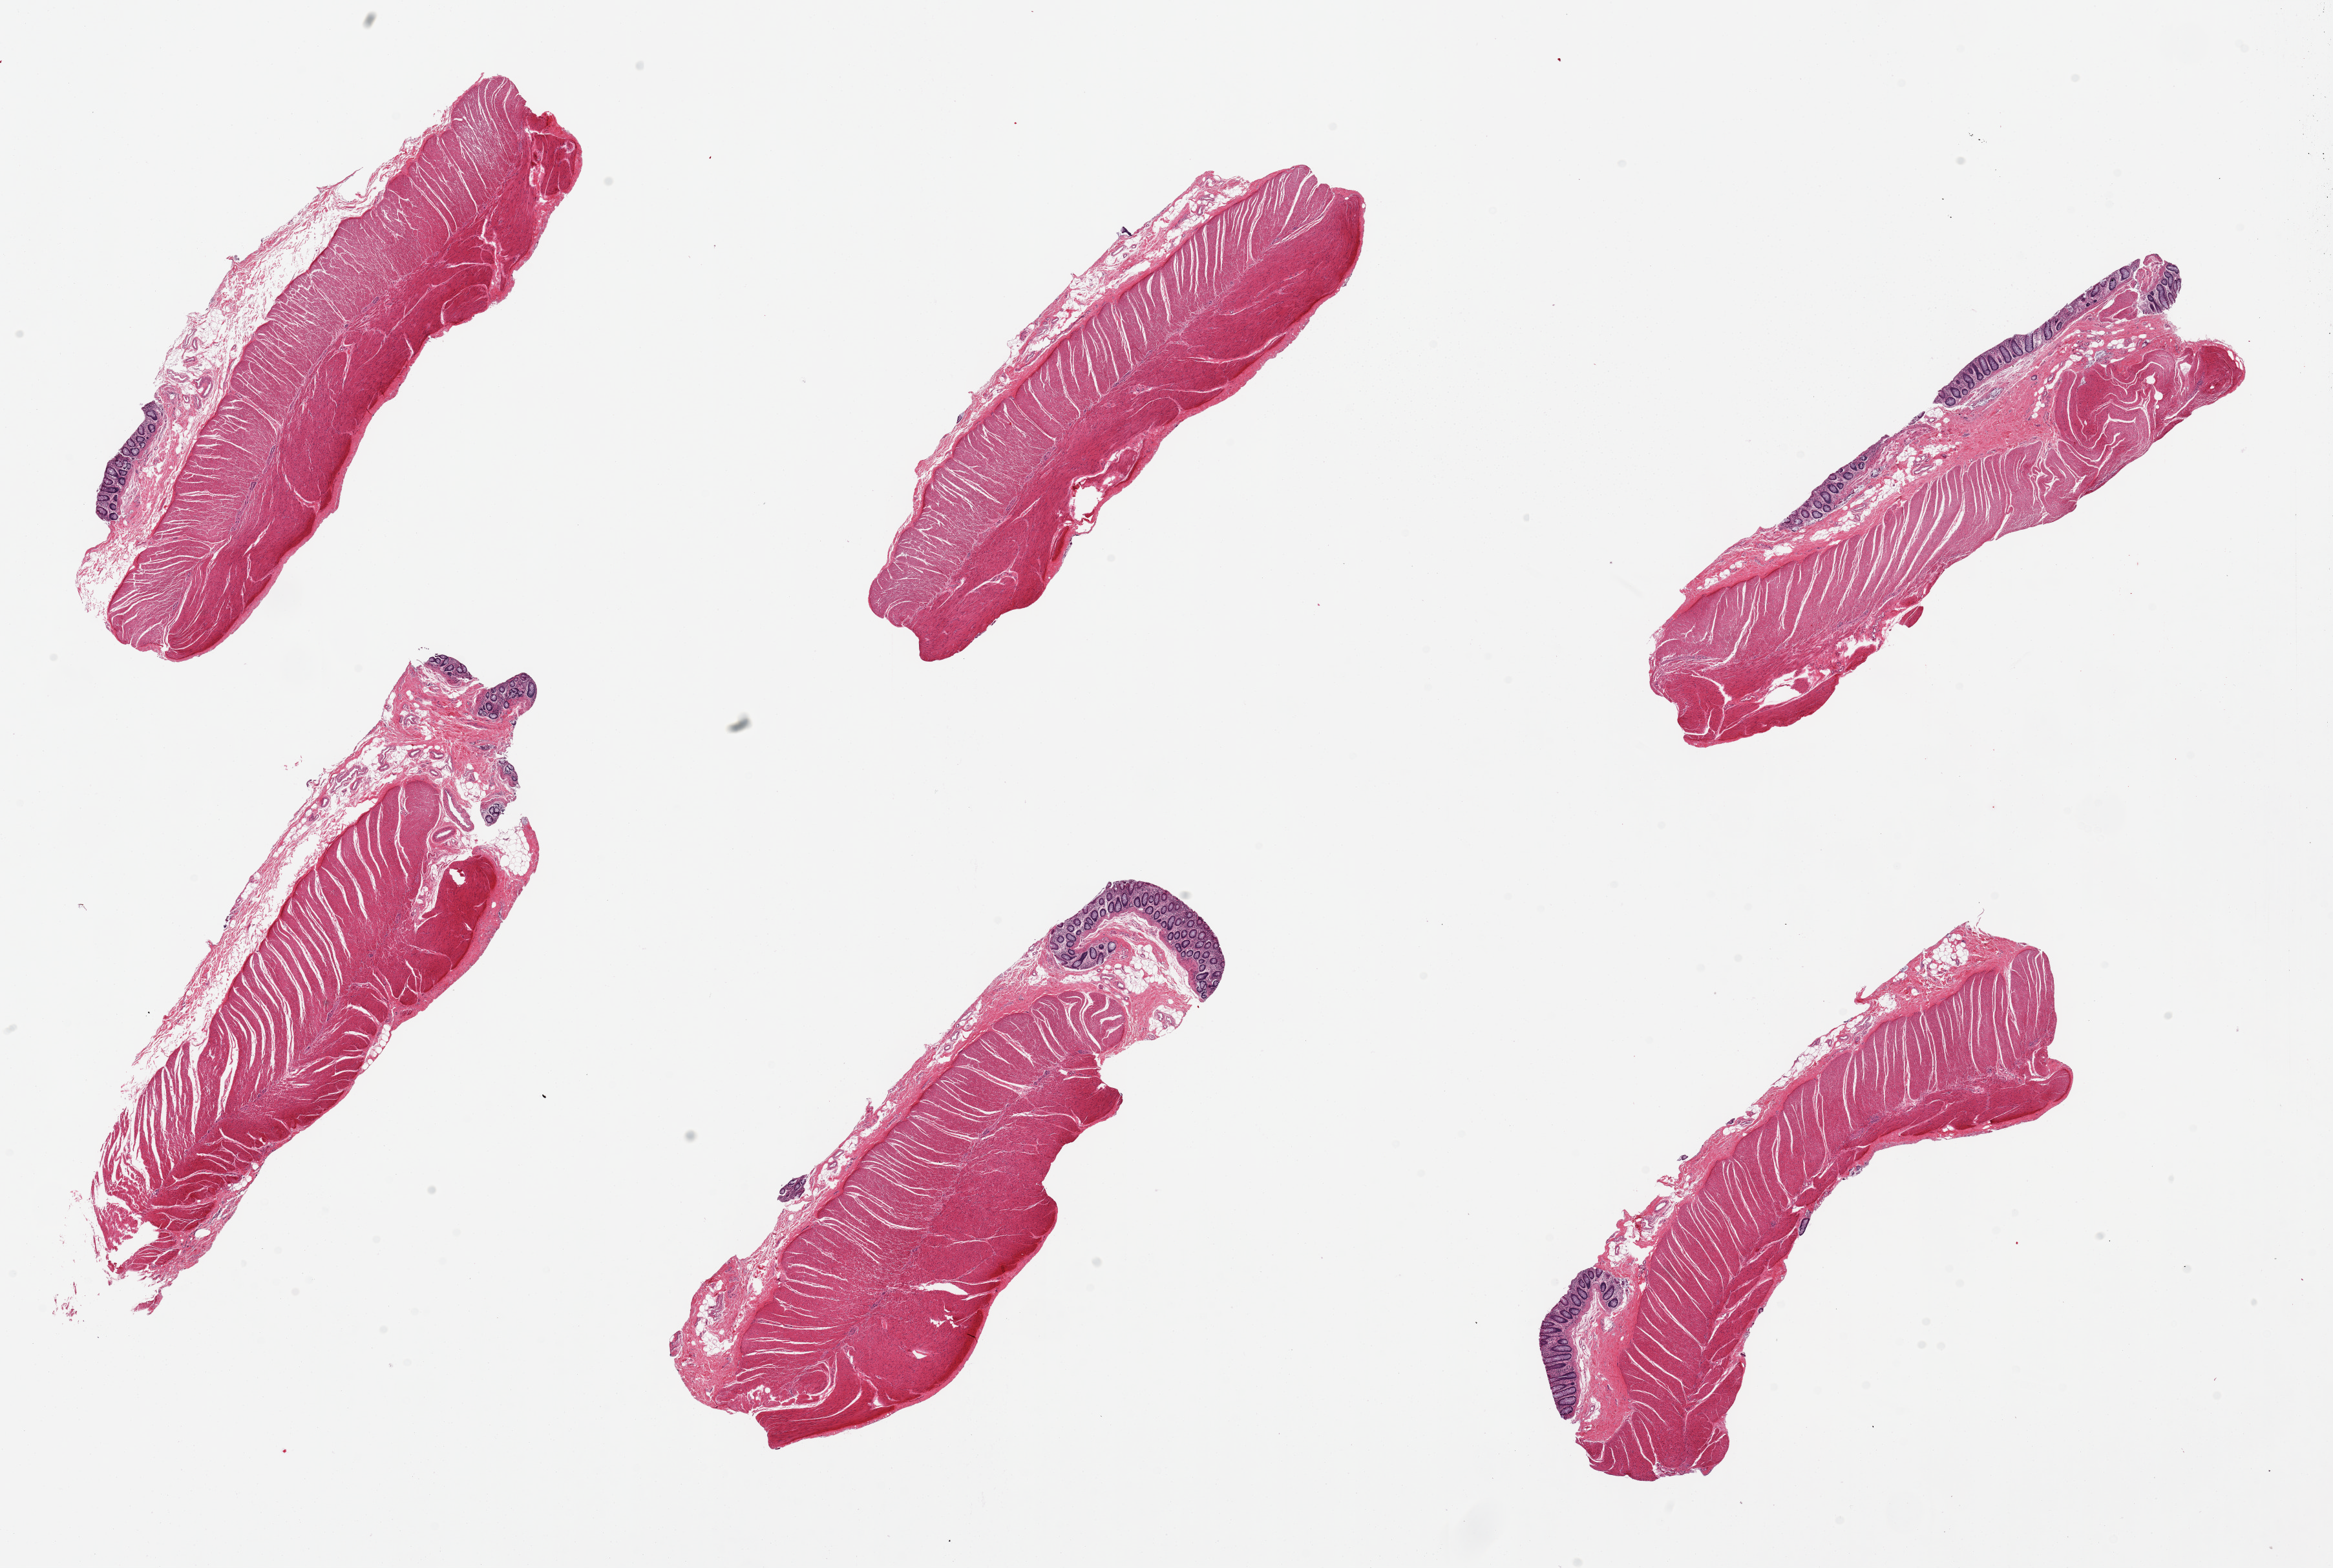
Digitized hematoxylin and eosin (H&E)-stained section, brightfield, shown as a low-resolution overview of the whole scanned area (about 28.5 x 19.2 mm). PAXgene-fixed, paraffin-embedded tissue. Sampled site (target tissue): sigmoid colon. Tissue donor sample. Donor: male.
* review note (as recorded): 6 pieces; from 8x3 to 9x3mm; remnants of mucosa on 5/6 pieces